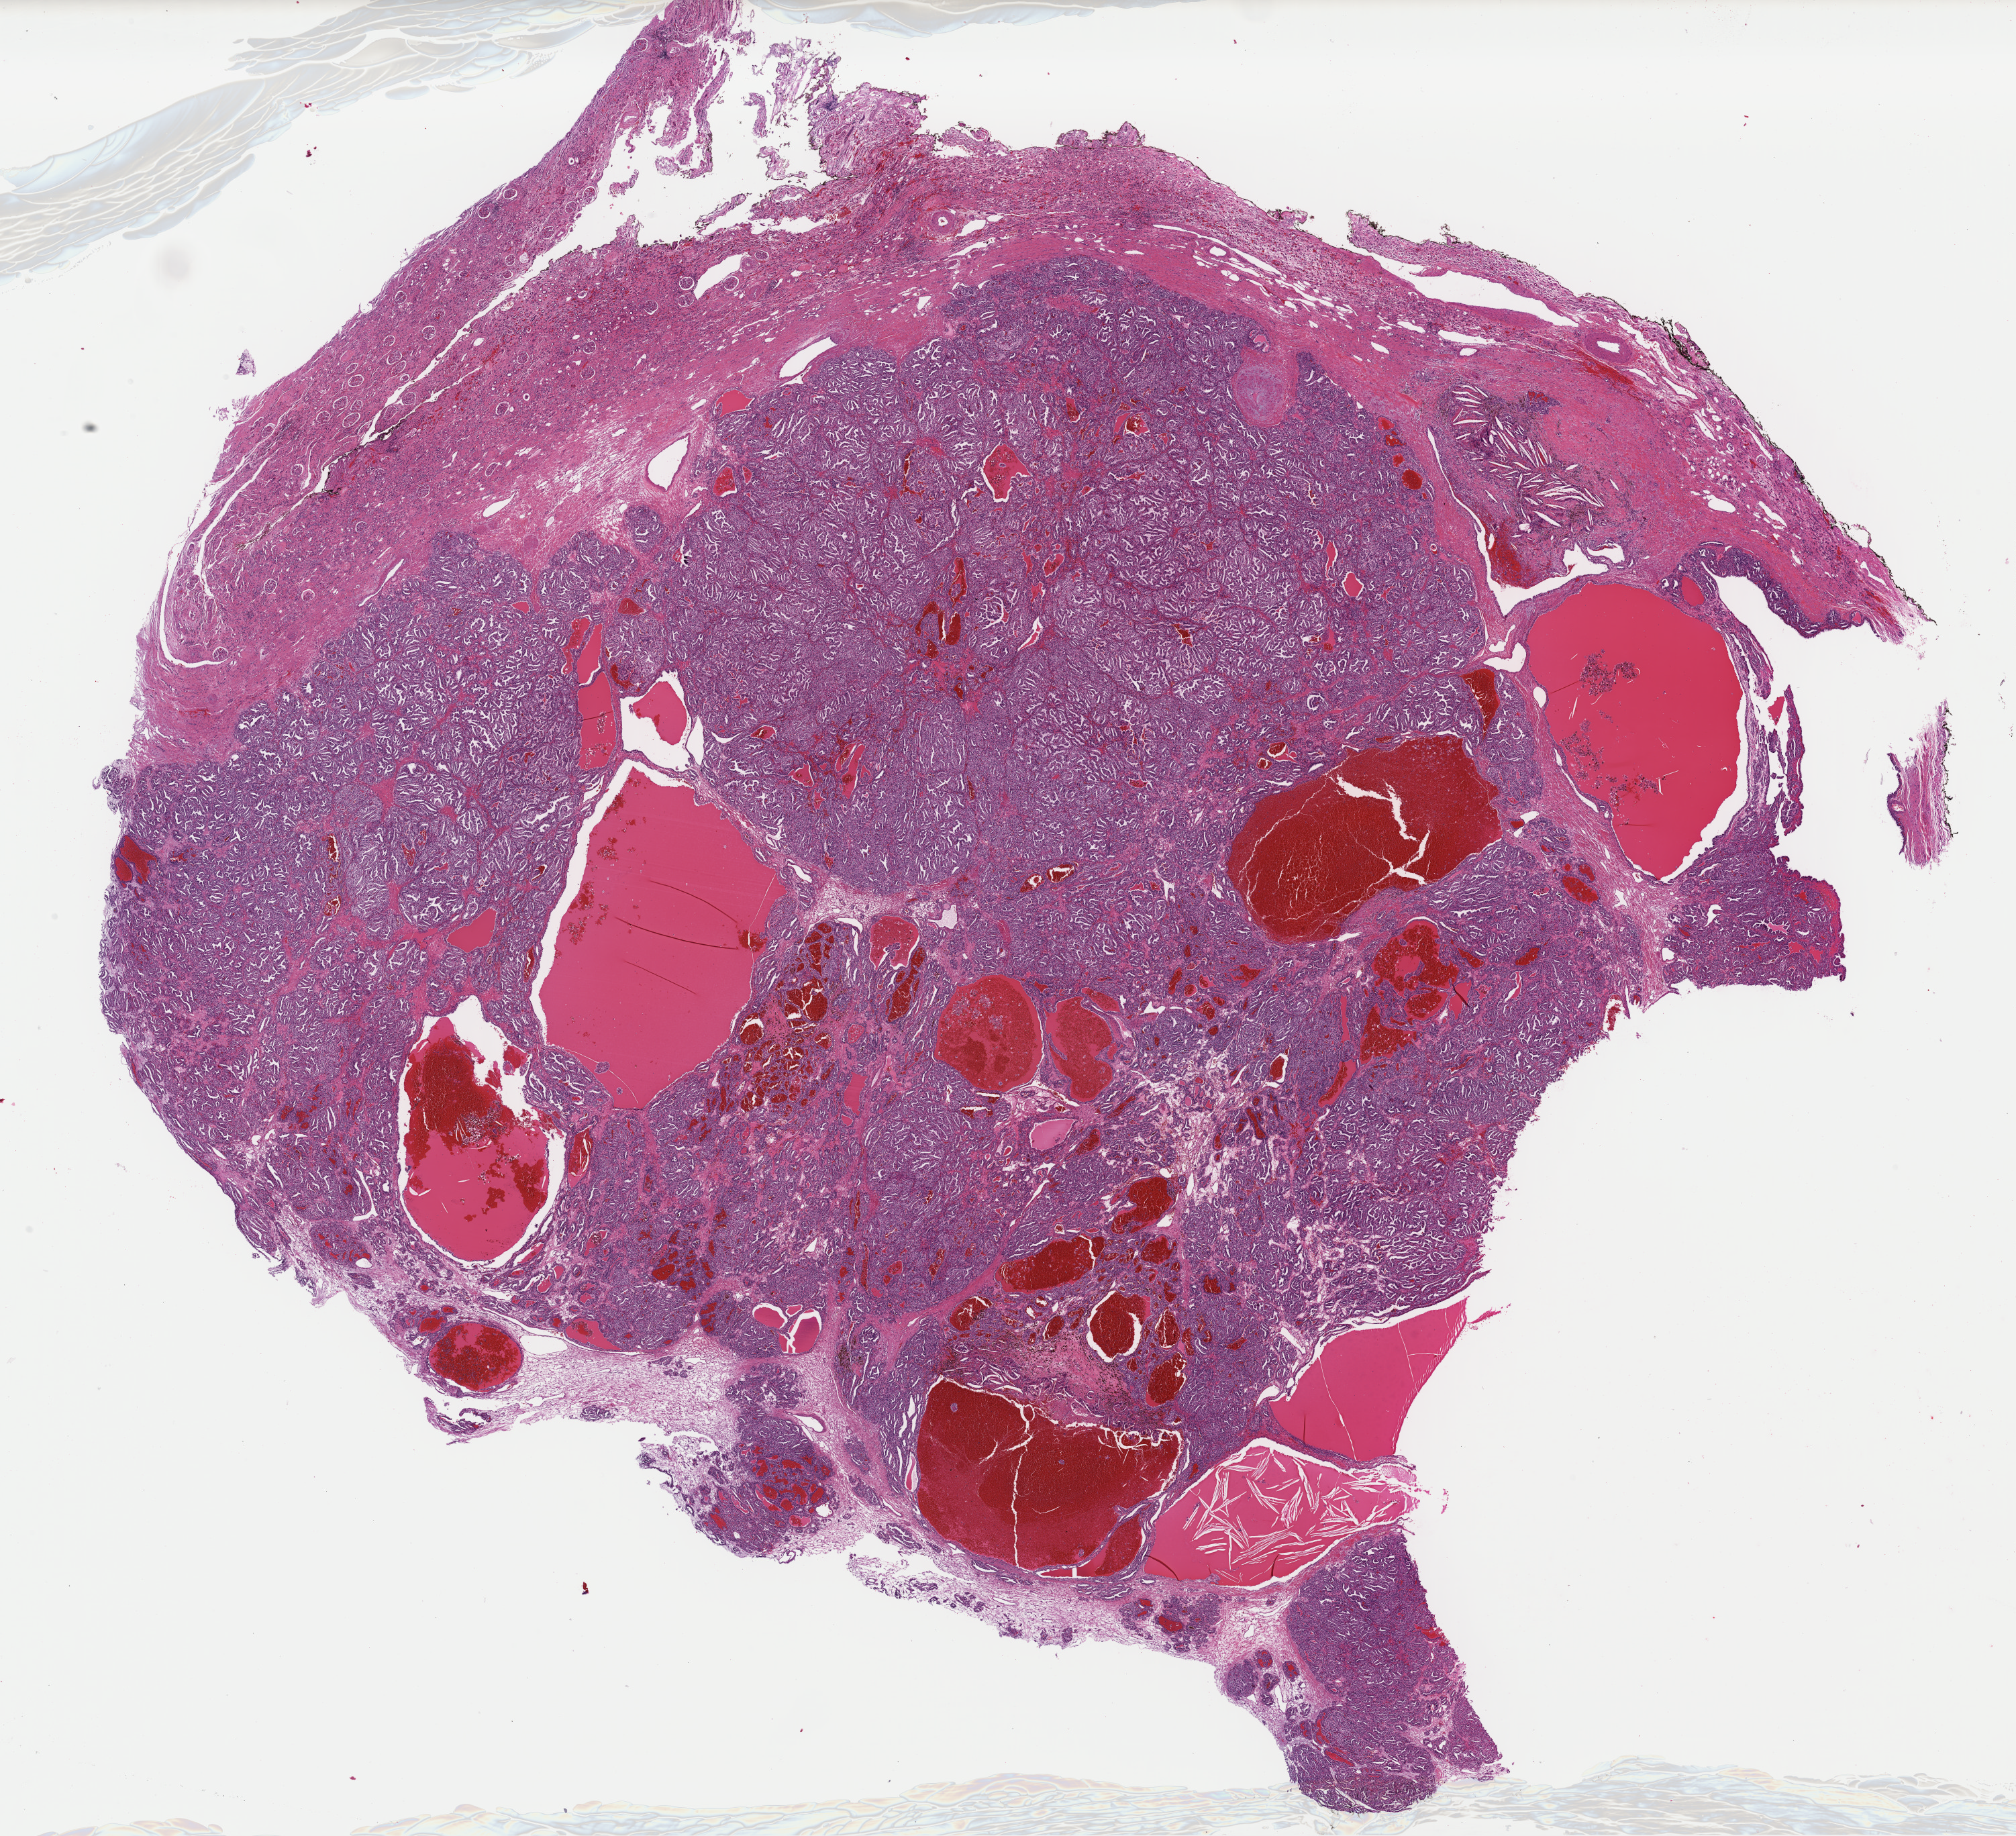
Digitized H&E-stained tissue section (whole slide), whole scanned area (about 23.7 x 21.6 mm) shown as a low-resolution overview, formalin-fixed paraffin-embedded (FFPE) diagnostic section, kidney, additional new primary tumour sample. Male, age 55 years at initial diagnosis.
This section: additional new primary tumour. Patient diagnosis: Clear cell adenocarcinoma, NOS.